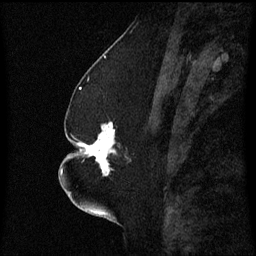
Breast MRI (dynamic contrast-enhanced), one sagittal slice. Position 26 of 60 along the scan axis. Dynamic contrast-enhanced series, image 2 of 3 at this slice position (ordered by acquisition). 1.5 T. TE 4.2 ms, TR 8.4 ms. 2.3 mm slice thickness. 256 × 256 image matrix, field of view 200 × 200 mm. Patient: female, 52 years. From the clinical record (not read from this slice): setting: breast cancer imaged before/during neoadjuvant chemotherapy; receptor status: HR-positive, HER2-negative.
Annotated regions visible in this slice (semi-automatic segmentation, software-assisted and operator-edited):
- analysis volume of interest (the breast-tissue region the enhancement analysis was run in; not a lesion): bounding box [x1, y1, x2, y2] px = [75, 122, 131, 177]
- tumour enhancement mask (voxels above the 70 % enhancement threshold inside the analysis volume of interest): [77, 122, 116, 177]